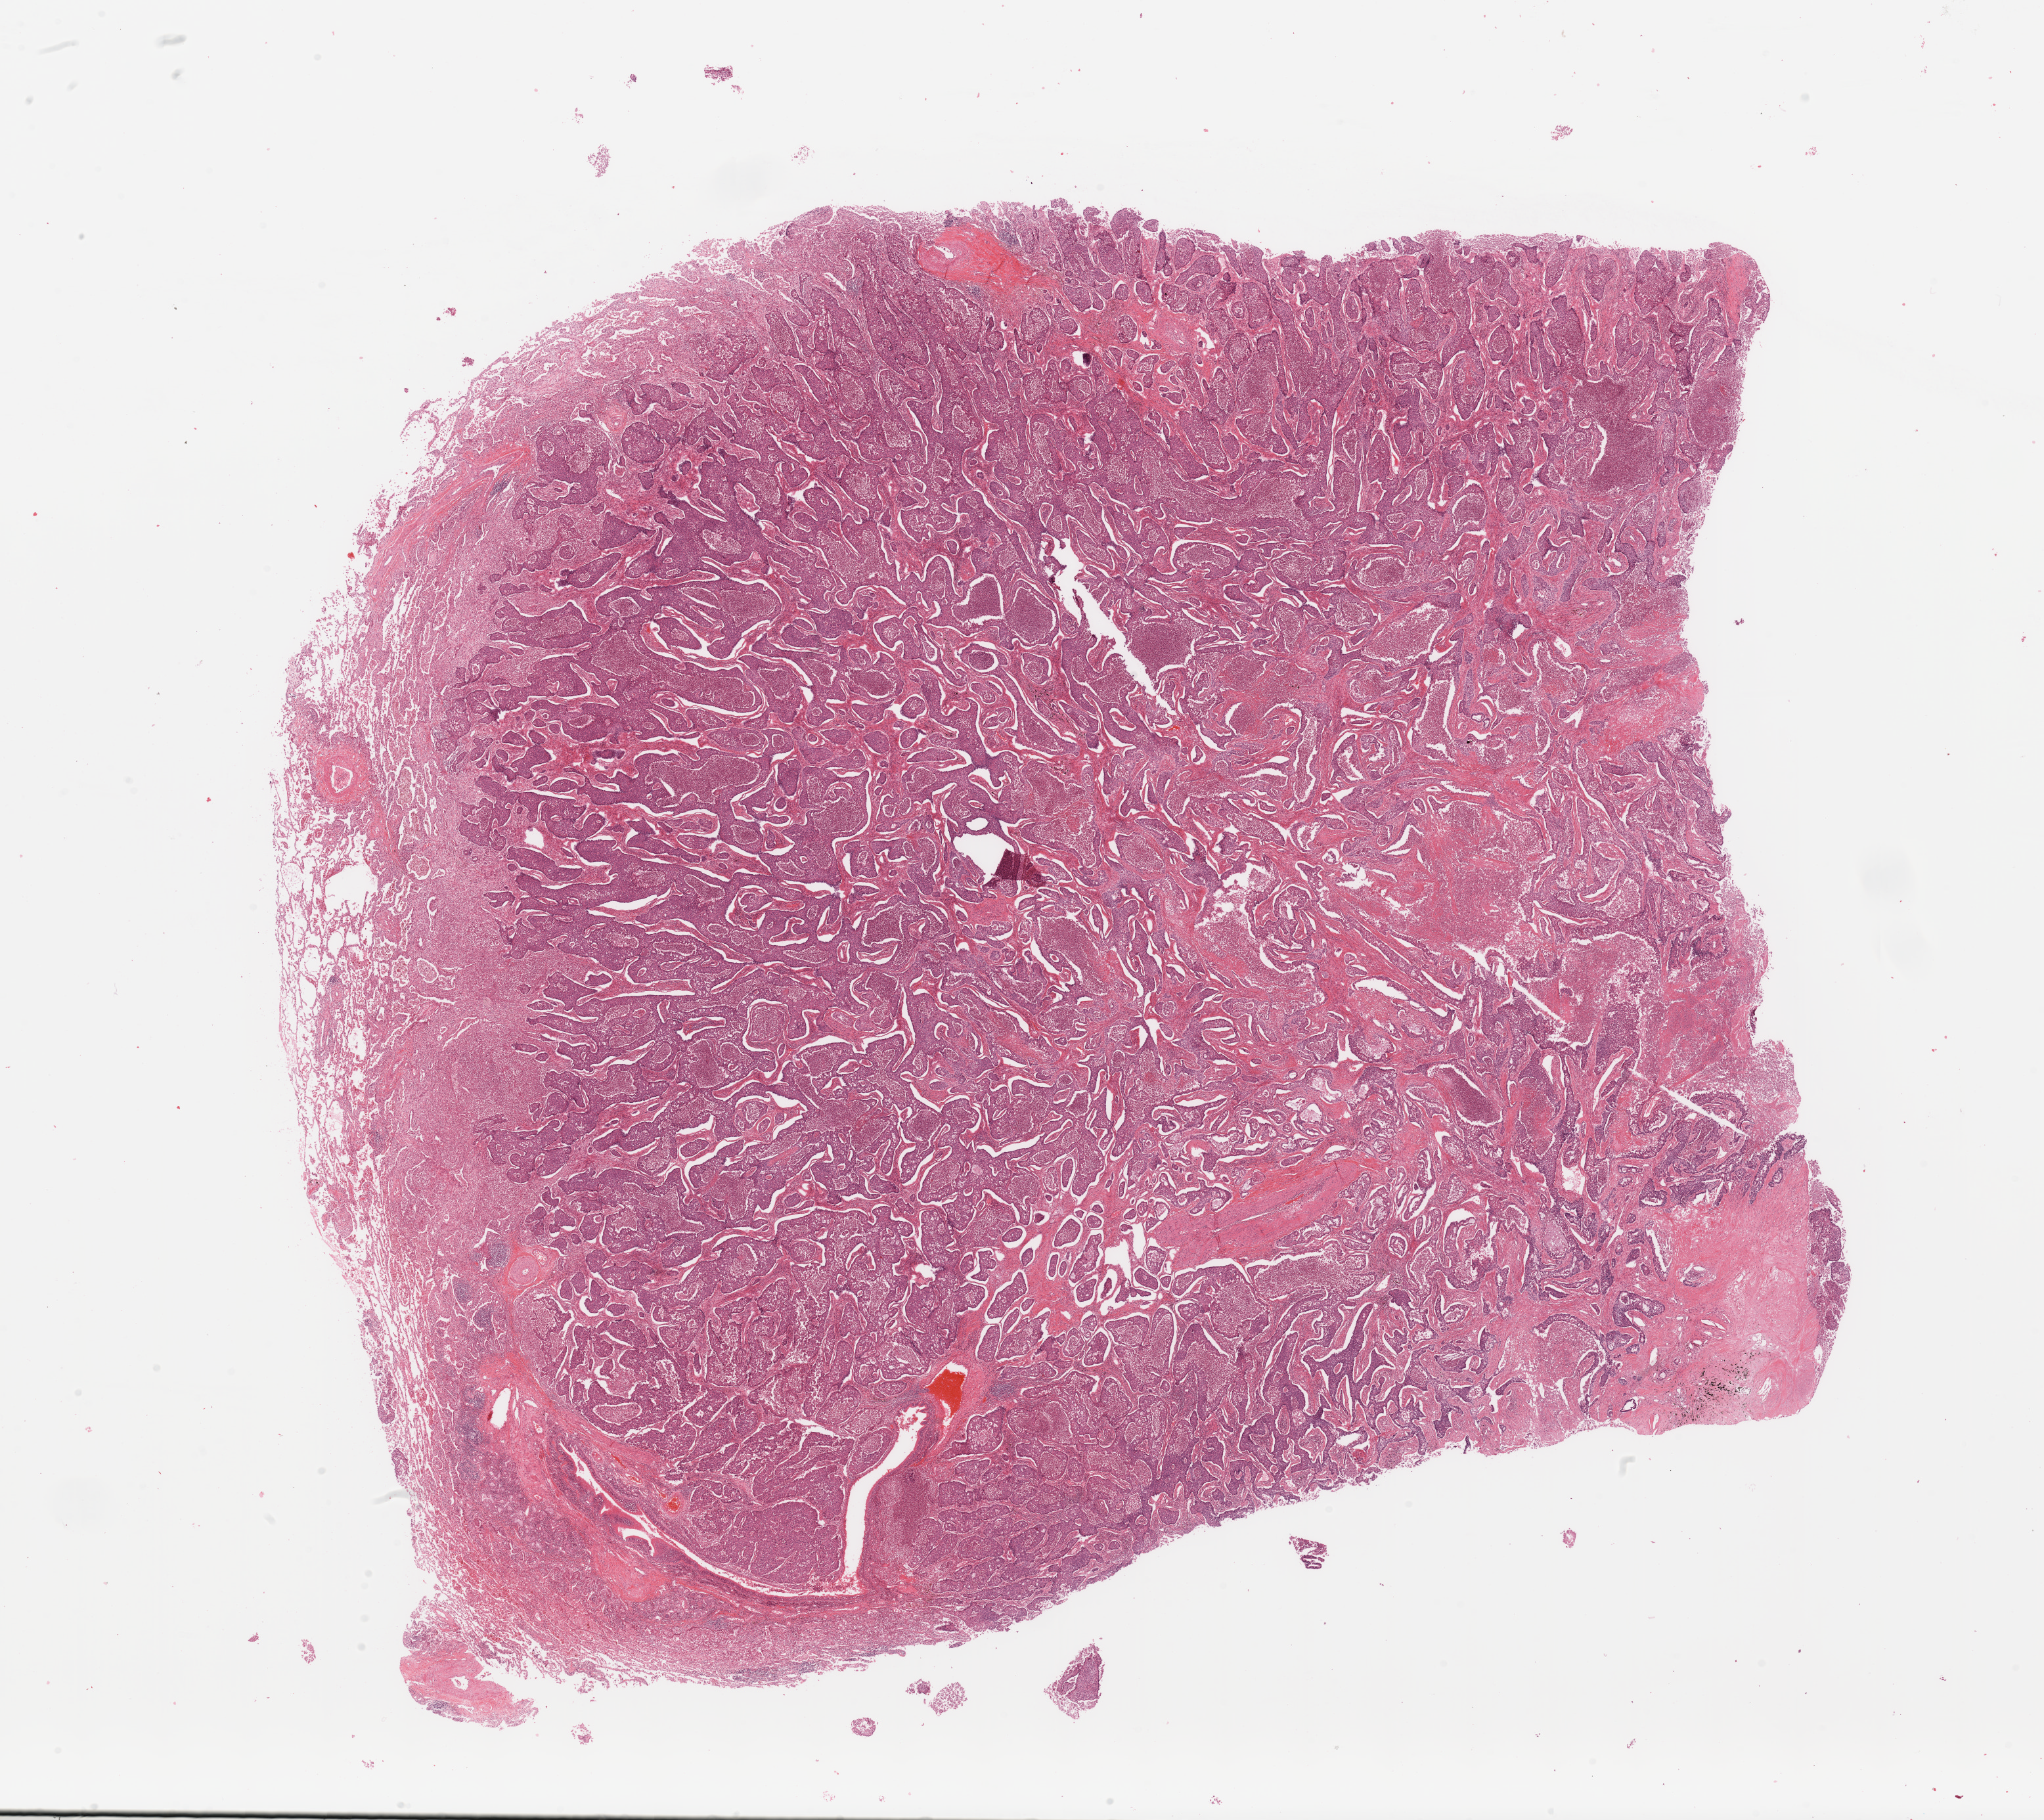
Whole-slide histology image, Hematoxylin and eosin (H&E) stained, low-resolution overview of the scanned area, about 24.6 x 21.9 mm, lung, tumour tissue. 58-year-old male patient. Histologic grade: G3 (poorly differentiated).
Histologic diagnosis: Adenocarcinoma, NOS. AJCC pathologic stage: IIIA.